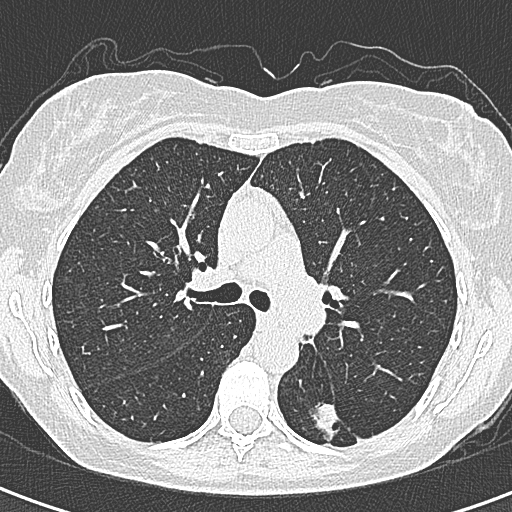
Chest CT (low-dose screening protocol), one axial image, baseline annual screen, lung window (W 1500 / L -600 HU), 1 mm slice thickness, slice 117 of 328 in the series. Female, age 58 years at enrolment. Former smoker at enrolment.
Expert-annotated lung lesion, bounding box <290,391,361,455> (left, top, right, bottom; pixels). The screening reader recorded 2 non-calcified nodules or masses ≥4 mm on this exam (left lower lobe, right lower lobe); which of them this box marks is not recorded. Official screen result: positive, change unspecified: nodule(s) >= 4 mm or enlarging nodule(s), mass(es), or other non-specific abnormalities suspicious for lung cancer. Lung cancer was diagnosed 22 days after this screen: adenocarcinoma, NOS, left lower lobe, moderately differentiated (G2), stage IA (AJCC 6th edition), 25 mm at pathology.